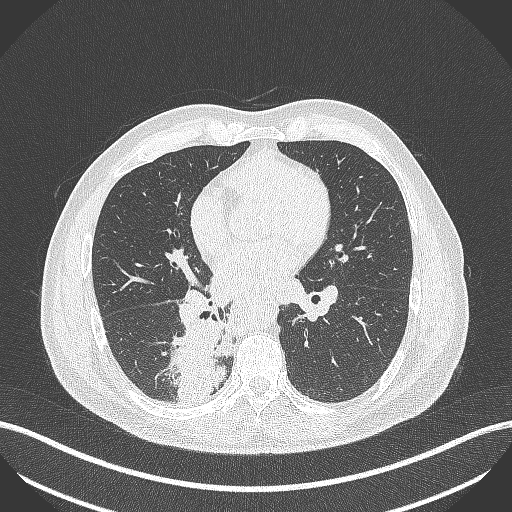
Chest CT, one axial slice. Position 224 of 451 along the scan axis. Reconstruction kernel B70f. Lung window (W 1500 / L -600 HU). 1 mm slice thickness. 512 × 512 image matrix, field of view 400 × 400 mm. Patient: male, 61 years. From the clinical record (not read from this slice): clinical TNM (as recorded): T1 N0 M0; histopathological grade: G3.
Annotated regions visible in this slice (bounding box drawn by a radiologist):
- lung tumour (recorded histology: small cell carcinoma): bounding box <171,318,226,399> (left, top, right, bottom; pixels)